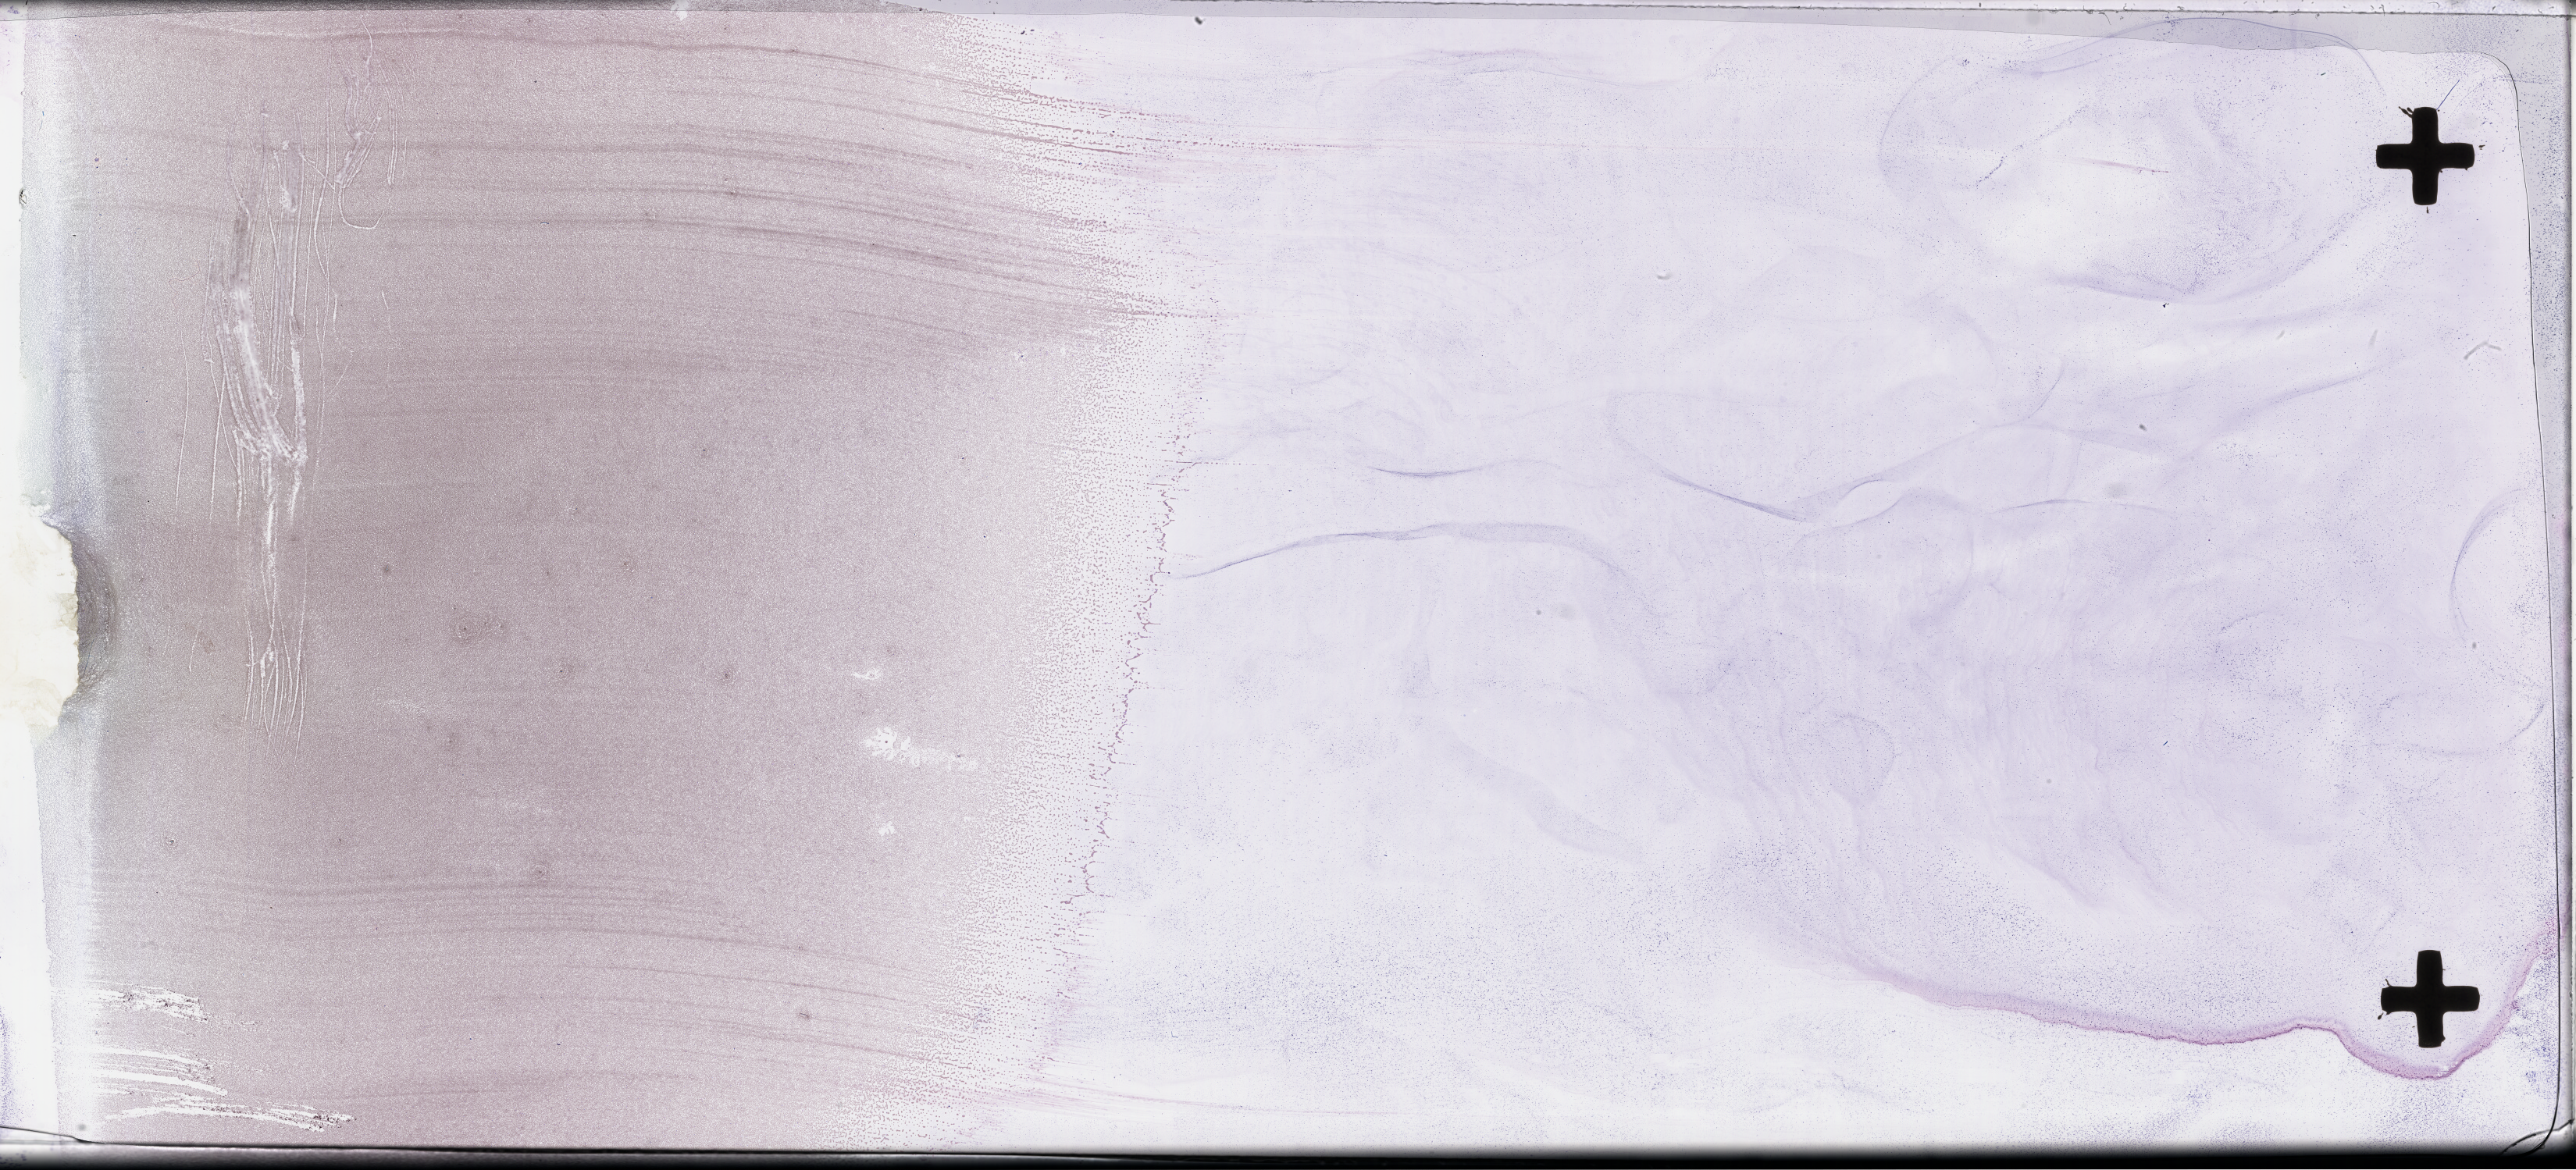
Whole-slide image of a whole blood smear, Wright–Giemsa stain, low-resolution overview of the scanned area, about 53.3 x 24.2 mm, smear from an EDTA sample, collected on treatment. Patient: female.
From a patient with: Plasma Cell Myeloma.